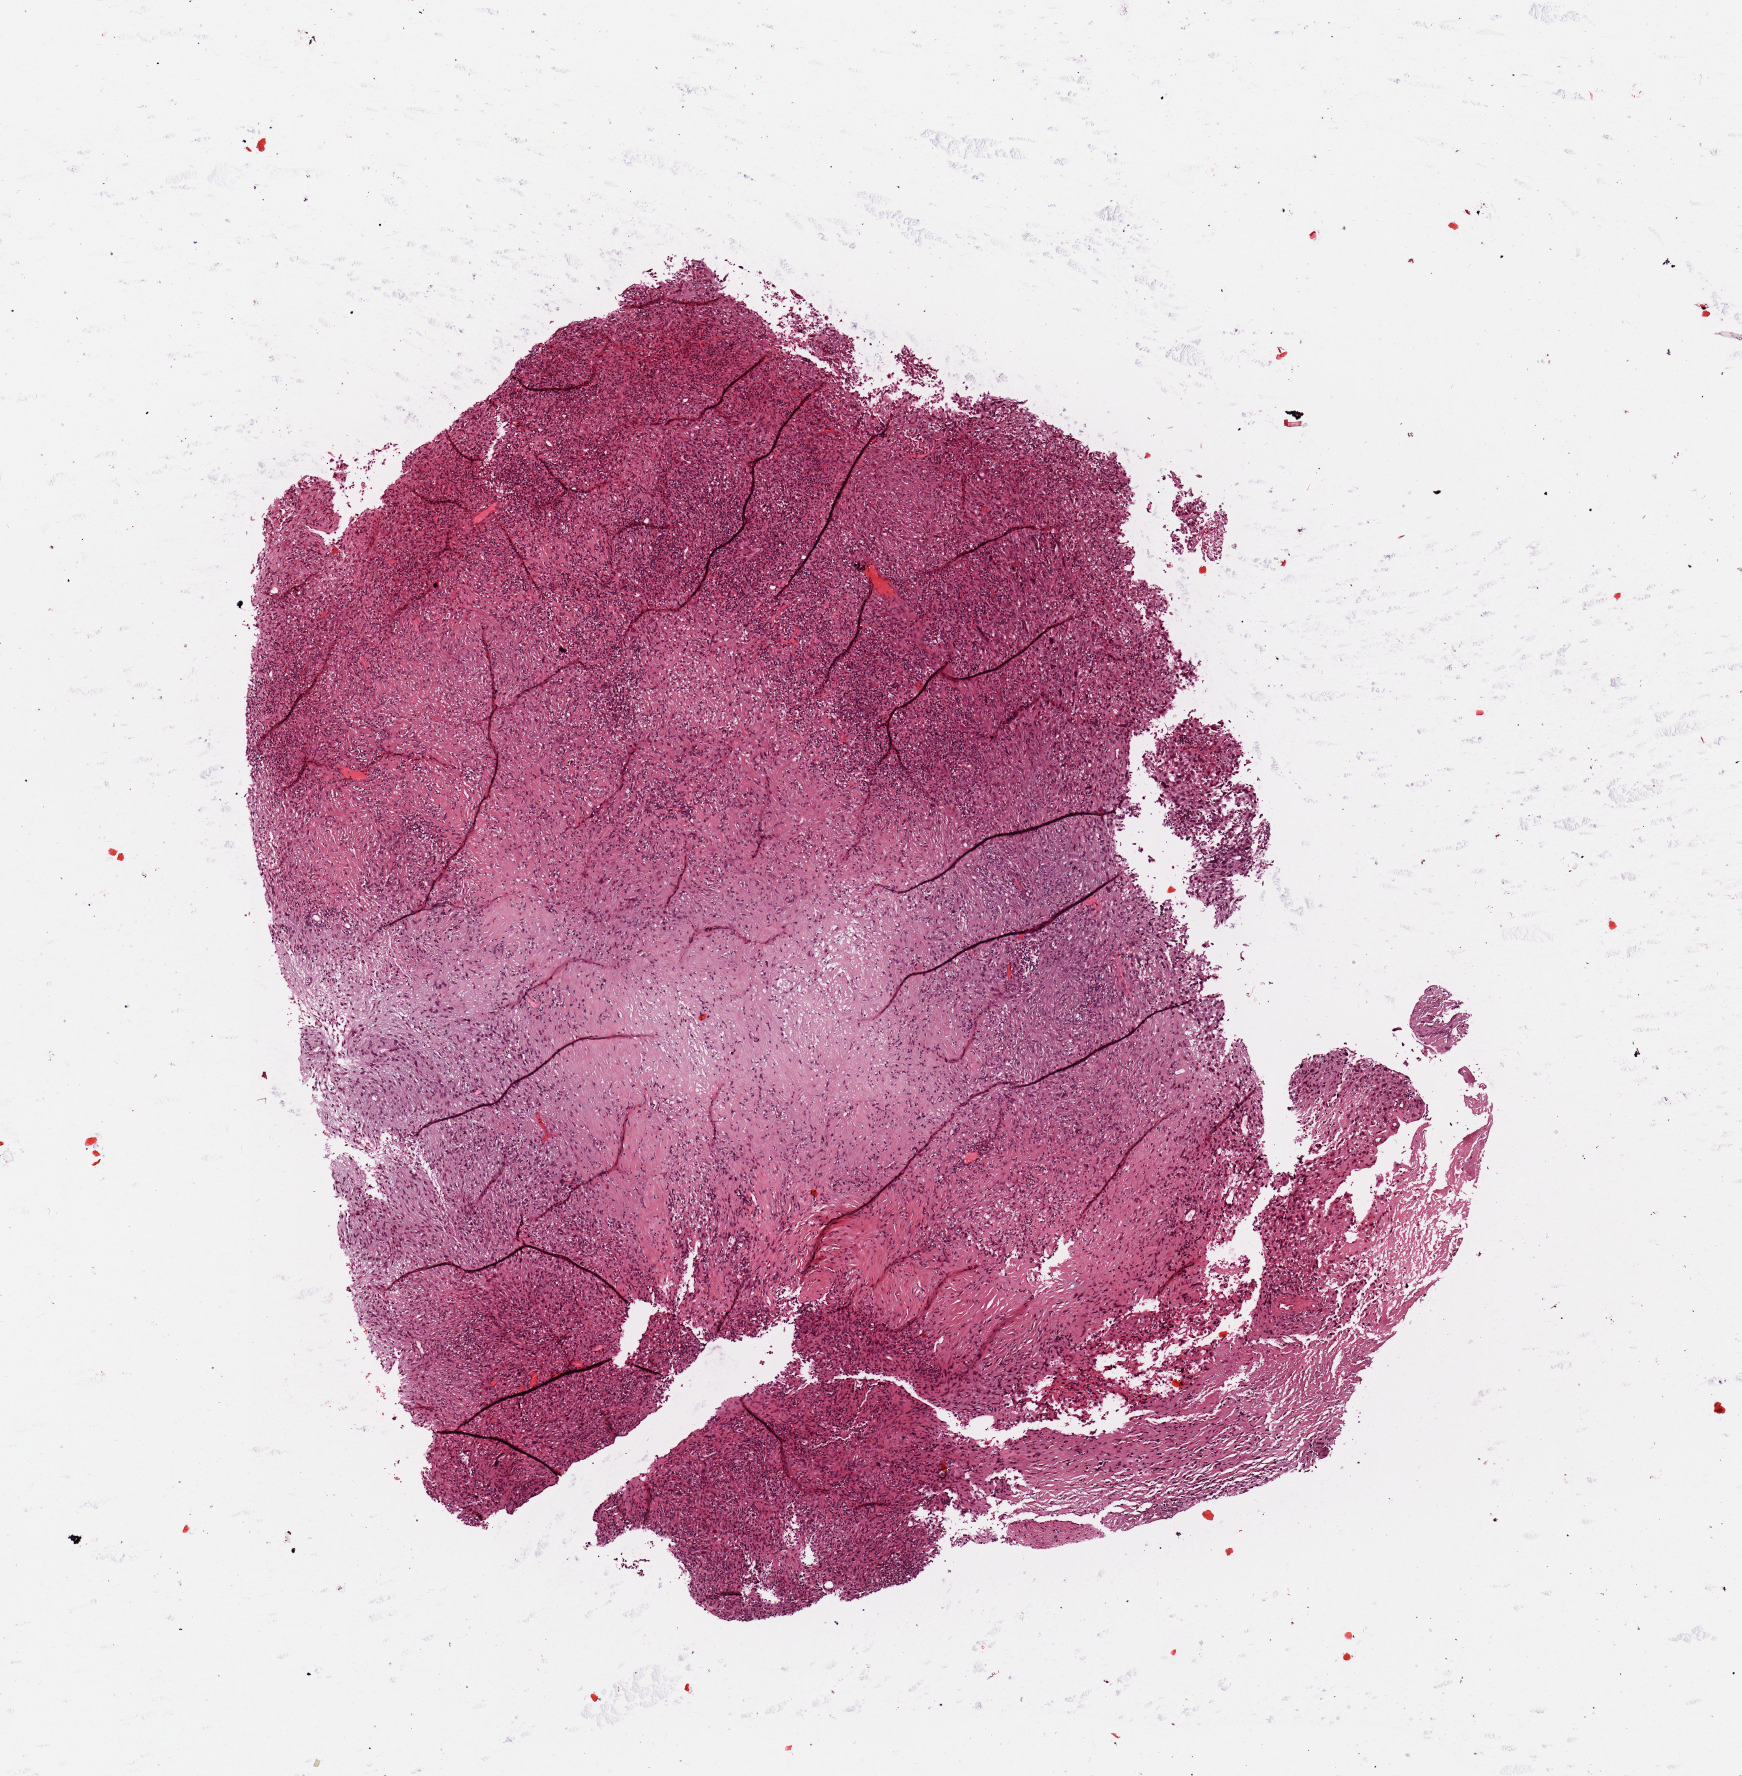
Digitized H&E tissue section (whole slide) — shown as a low-resolution overview of the whole scanned area (about 6.9 x 7.0 mm). Tumour tissue sample, brain. Female, 63 y/o.
Diagnosis: Glioblastoma.